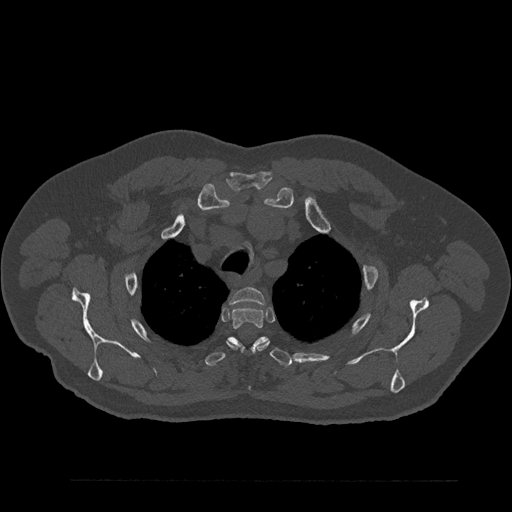
CT including the spine, one axial slice. Position 676 of 797 along the scan axis. Reconstruction kernel Br40s/3. 120 kVp. Bone window (W 1800 / L 400 HU). 0.5 mm slice thickness. 512 × 512 image matrix, field of view 430 × 430 mm. Male patient, age 61 years. Case-level facts recorded for this patient, not image findings: primary cancer: prostate.
Outlined on this slice (semi-automatically segmented with operator editing):
- T2 vertebra: bounding box <231,288,266,304> (left, top, right, bottom; pixels)
- T3 vertebra: <227,307,269,354>
- T4 vertebra: <205,336,292,367>